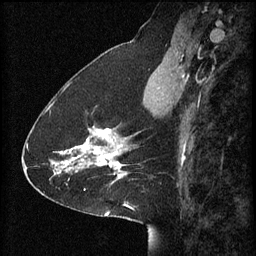
Breast MRI (dynamic contrast-enhanced), one sagittal slice; 3 images stored at this slice position (order not interpretable as contrast timing); 1.5 T; TE 4.2 ms, TR 8.2 ms; 2 mm slice thickness; 256 × 256 image matrix. Patient: female, 41 years.
Structures marked on this image (semi-automatic segmentation, software-assisted and operator-edited):
- analysis volume of interest (the breast-tissue region the enhancement analysis was run in; not a lesion): bounding box <58,114,128,181> (left, top, right, bottom; pixels)
- tumour enhancement mask (voxels above the 70 % enhancement threshold inside the analysis volume of interest): <58,128,128,181>